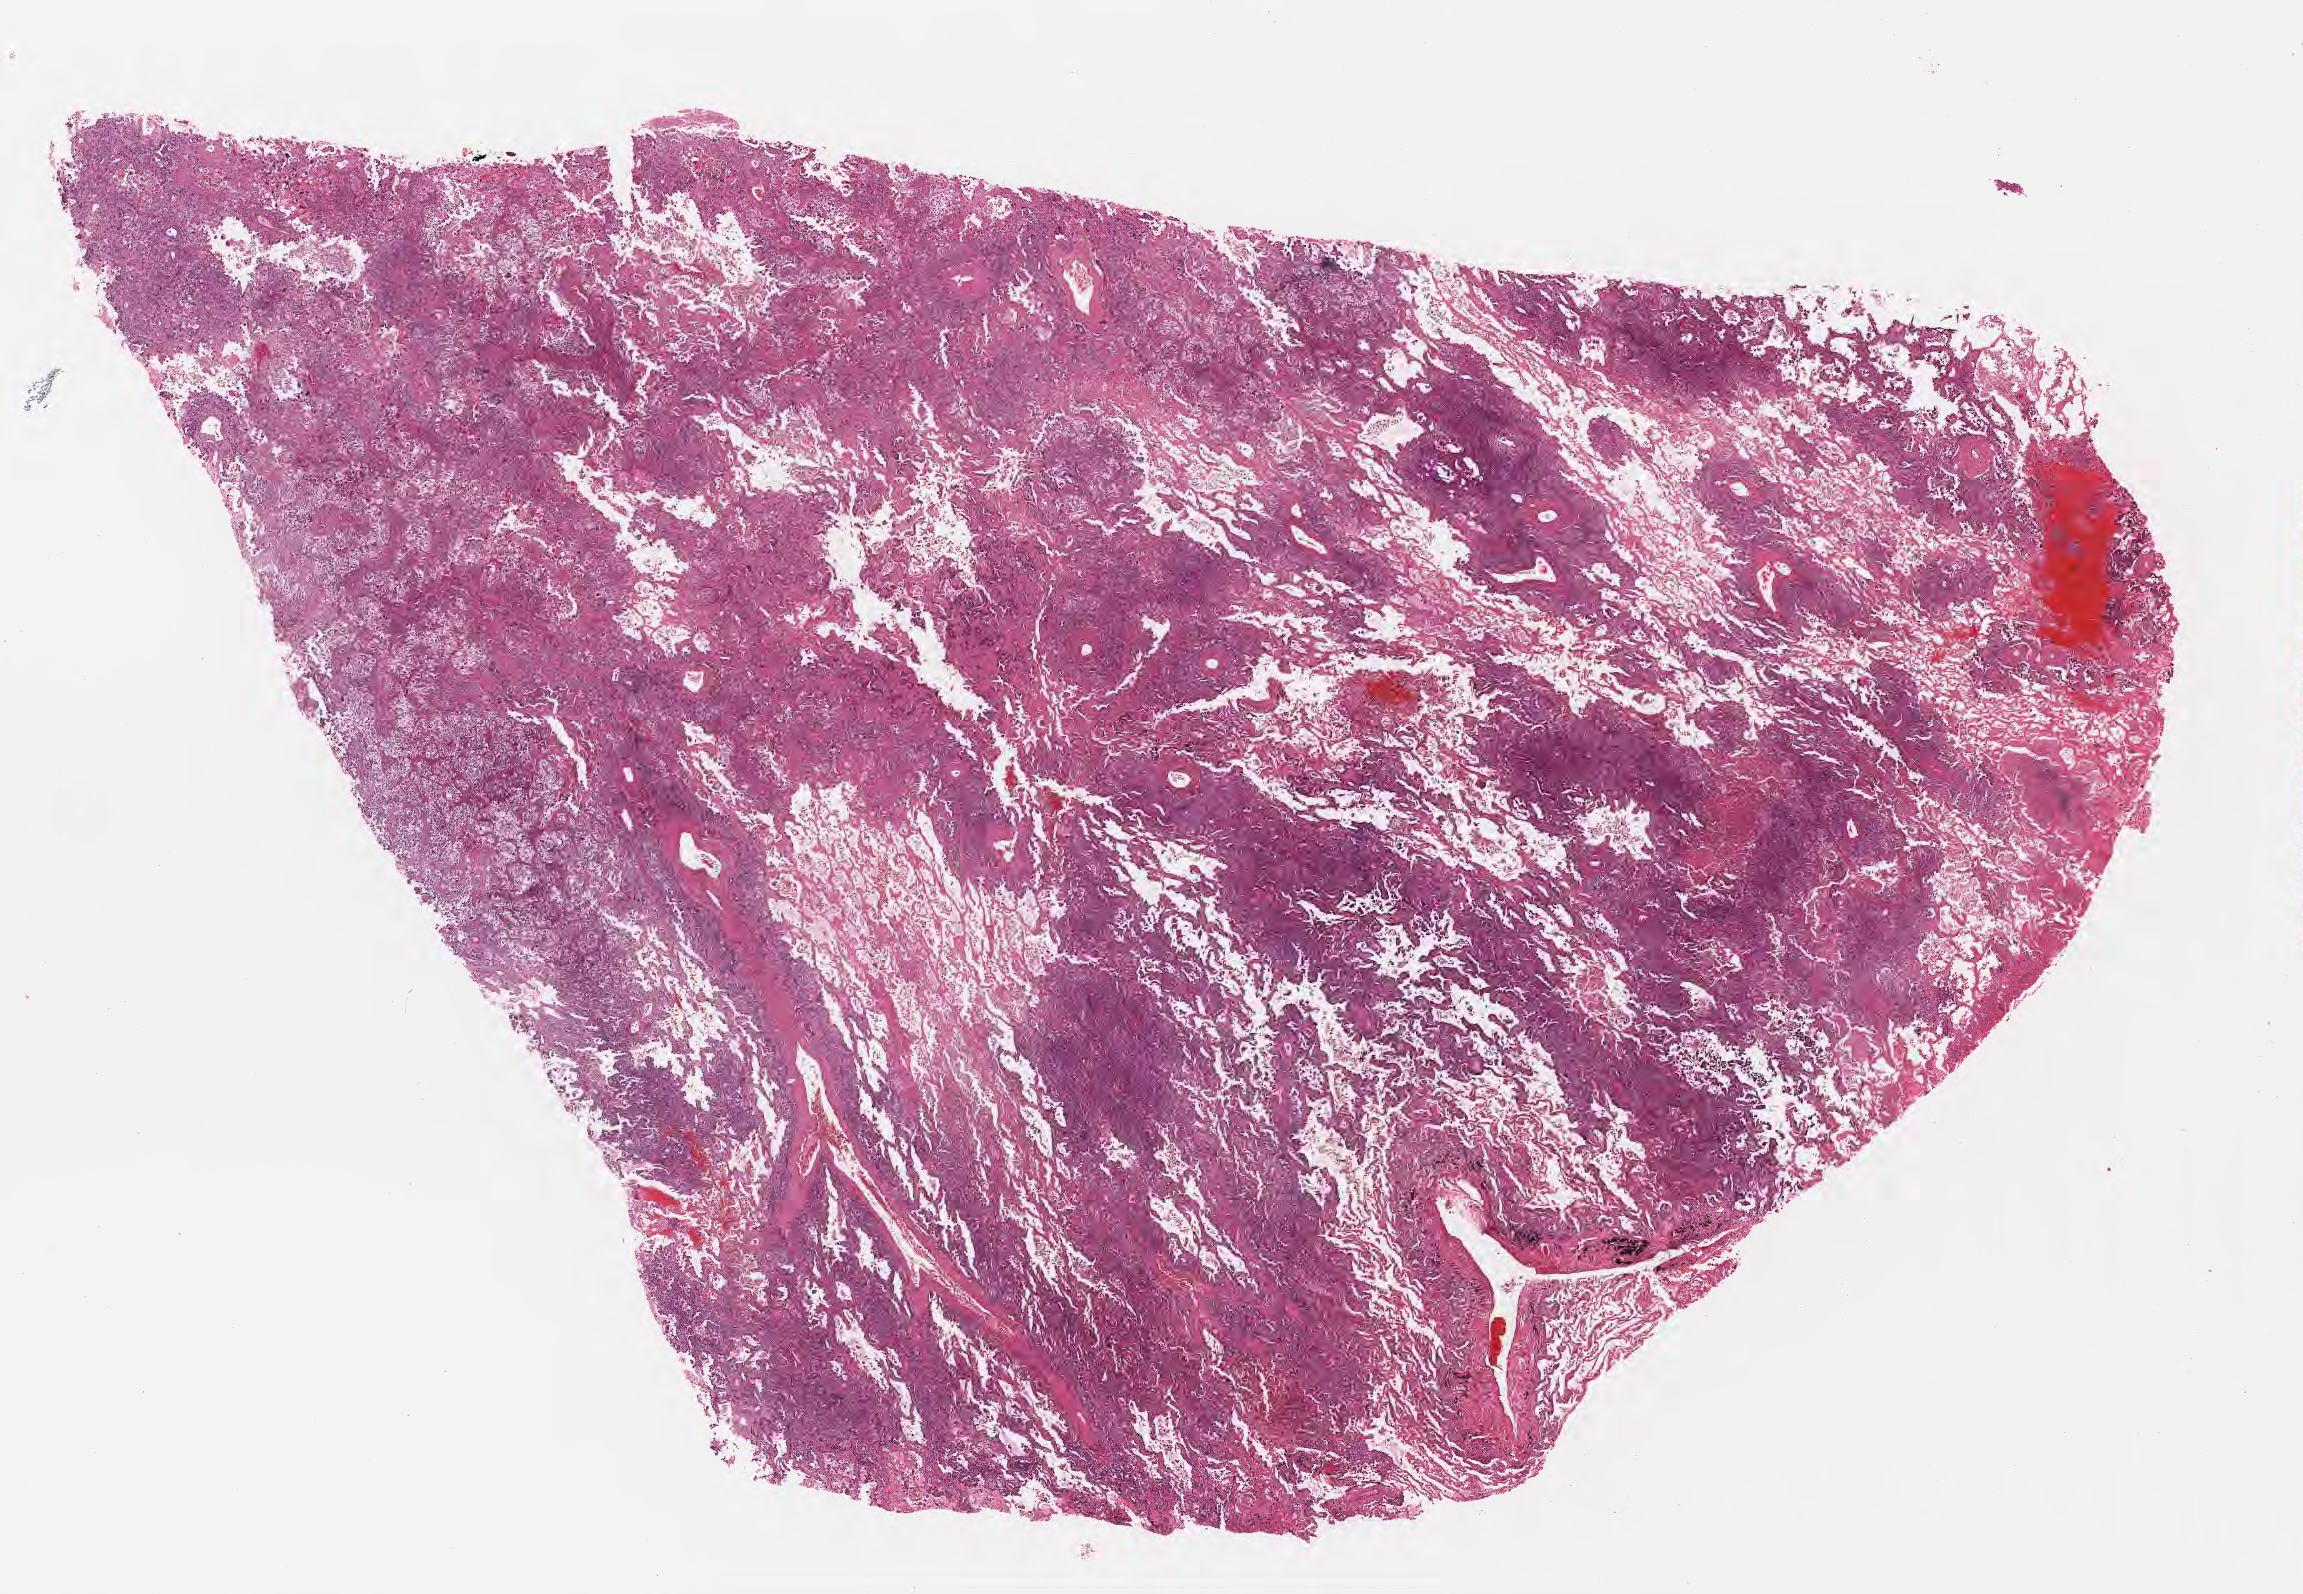
Digitized H&E-stained section, low-resolution overview of the scanned area, about 18.6 x 12.9 mm. FFPE section. Specimen: primary tumor. Anatomic site: upper lobe of left lung. Patient male; age 65 years. Slide review estimates, as recorded: tumor cells 75%, tumor nuclei 75%, stromal cells 20%, necrosis 2%, normal cells 3%. Infiltration values recorded for this section: lymphocyte infiltration 3%, monocyte infiltration 5%, neutrophil infiltration 6%.
- histologic diagnosis: Acinar cell carcinoma
- AJCC pathologic stage: Stage IIB